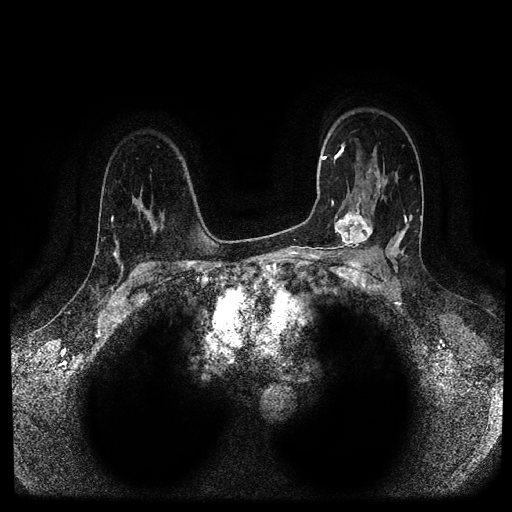
Breast MRI (dynamic contrast-enhanced, multi-phase), one axial slice. Position 71 of 116 along the scan axis. Dynamic contrast-enhanced series, time point 2 of 5 at this slice position (early post-contrast). 1.5 T. TE 2.6 ms, TR 5.3 ms. 512 × 512 image matrix, field of view 350 × 350 mm. Female patient, age 44 years.
Outlined on this slice (semi-automatically segmented with operator editing):
- breast lesion (labelled 'tumour' in the annotation; benign lesions carry a separate 'benign' label): bounding box (x1, y1, x2, y2) in pixels: (334, 196, 373, 250)